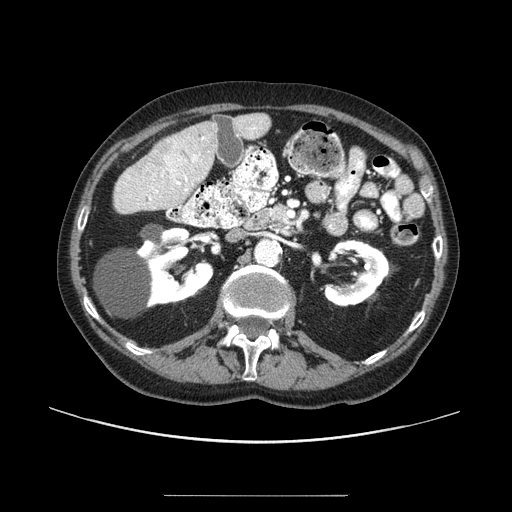
Contrast-enhanced abdominal CT (liver protocol), one axial slice. Slice 35 of 91 in the series (ordered by position). Reconstruction kernel STANDARD. One of 2 acquisitions stored at this slice position. Soft-tissue window (W 400 / L 40 HU). 512 × 512 image matrix, field of view 400 × 400 mm. Case-level facts recorded for this patient, not image findings: diagnosis: hepatocellular carcinoma (patient treated with transarterial chemoembolisation; whether this scan precedes or follows treatment is not stated here); TNM stage (as recorded): Stage-I; Child-Pugh class: A.
Outlined on this slice (semi-automatic segmentation, software-assisted and operator-edited):
- liver parenchyma outside the tumour (the mass and vessels are separate outlines, so this box may not span the whole liver): bounding box <172,114,270,189> (left, top, right, bottom; pixels)
- mass: <149,139,189,177>
- liver vessels: <191,127,257,180>